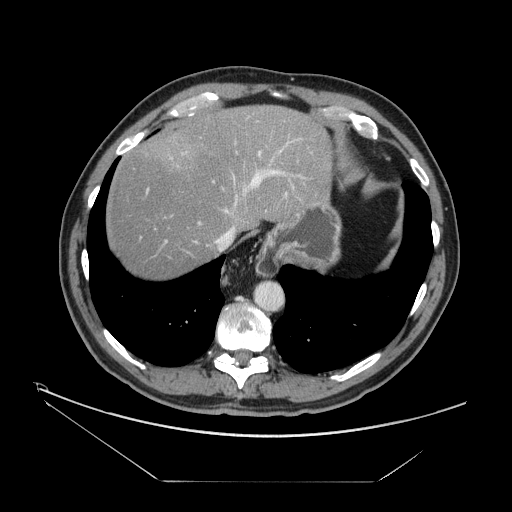
Contrast-enhanced abdominal CT, one axial slice. Slice 132 of 161 in the series (ordered by position). Reconstruction kernel STANDARD. Intravenous contrast given. Soft-tissue window (W 400 / L 40 HU). 2.5 mm slice thickness. 512 × 512 image matrix, field of view 440 × 440 mm. Male patient, age 65 years. From the clinical record (not read from this slice): diagnosis: colorectal cancer liver metastases, imaged before liver resection; multiple liver metastases: yes; largest metastasis: 4.2 cm; disease in both lobes: yes.
Structures marked on this image (expert manual segmentation):
- hepatic veins: bounding box (x1, y1, x2, y2) in pixels: (207, 150, 283, 252)
- liver: (105, 105, 331, 279)
- planned liver remnant (the part of the liver to remain after resection): (105, 105, 331, 279)
- portal vein (with intrahepatic branches): (147, 114, 304, 244)